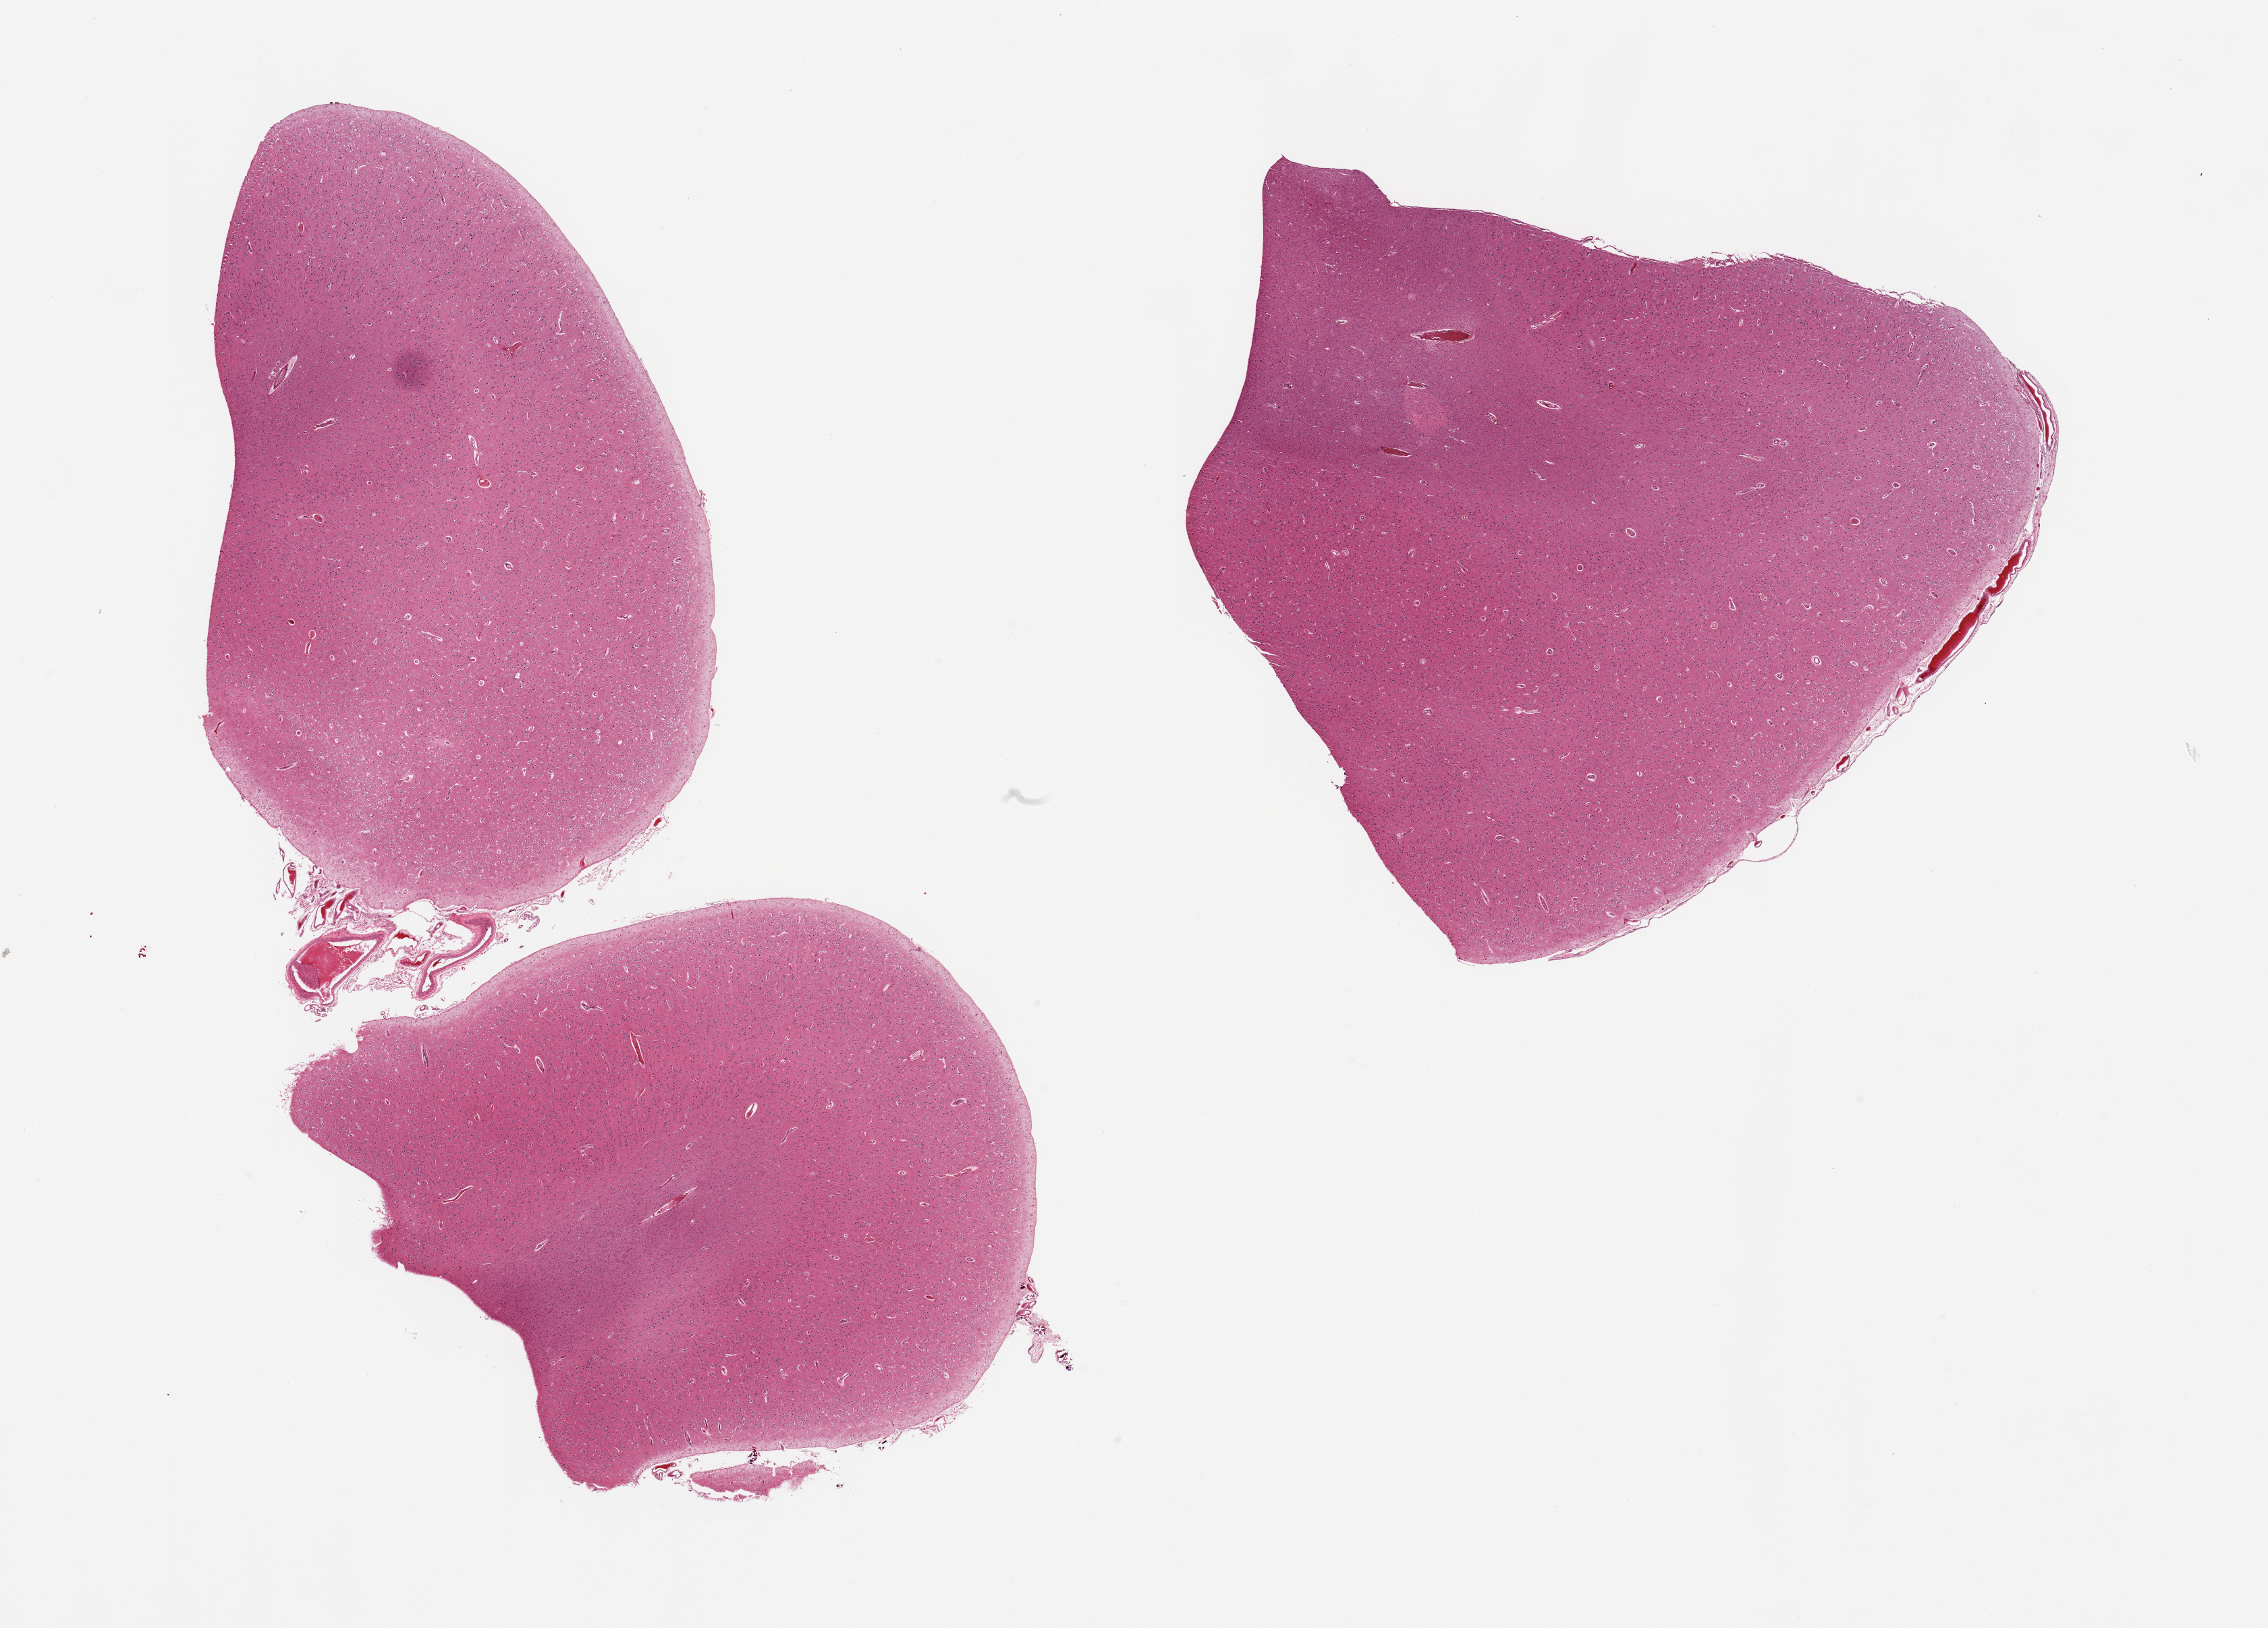
Whole-slide image, H&E stain, brightfield, shown as a low-resolution overview of the whole scanned area (about 26.6 x 19.1 mm, slide scanned at 20x), PAXgene-fixed paraffin-embedded (PFPE) section, section of cerebral cortex (target tissue), tissue donor sample. Donor: male.
Pathologist's review note for this sample: 2 pieces, no abnormalities2.